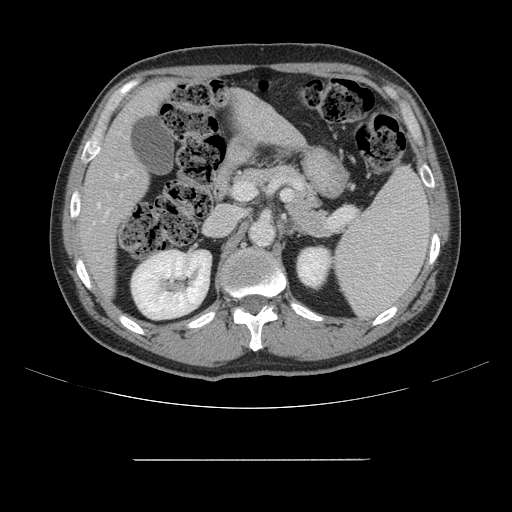
Contrast-enhanced abdominal CT, one axial slice; position 81 of 164 along the scan axis; 120 kVp; intravenous contrast given; soft-tissue window (W 400 / L 40 HU); 2.5 mm slice thickness; 512 × 512 image matrix, field of view 404 × 404 mm. Male patient, age 54 years. From the clinical record (not read from this slice): diagnosis: colorectal cancer liver metastases, imaged before liver resection.
Outlined on this slice (manually delineated by an expert):
- hepatic veins: bounding box (x1, y1, x2, y2) in pixels: (97, 173, 119, 207)
- liver: (82, 85, 298, 291)
- planned liver remnant (the part of the liver to remain after resection): (82, 85, 168, 291)
- portal vein (with intrahepatic branches): (106, 211, 109, 216)